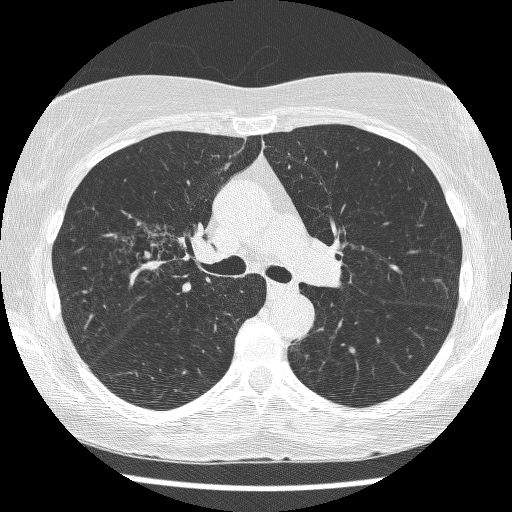
Low-dose screening chest CT, axial slice. Baseline annual screen. Lung window (W 1500 / L -600 HU). 120 kVp. Female, age 64 years at enrolment. Former smoker at enrolment.
- Expert-annotated lung lesion, bounding box [x1, y1, x2, y2] px = [125, 221, 204, 291].
- The screening reader recorded 3 non-calcified nodules or masses ≥4 mm on this exam; which of them this box marks is not recorded.
- Official screen result: positive, change unspecified: nodule(s) >= 4 mm or enlarging nodule(s), mass(es), or other non-specific abnormalities suspicious for lung cancer.
- Later outcome: lung cancer diagnosed 735 days after this screen — adenocarcinoma, NOS, right upper lobe, right middle lobe, right hilum, stage IV (AJCC 6th edition), 85 mm at pathology.